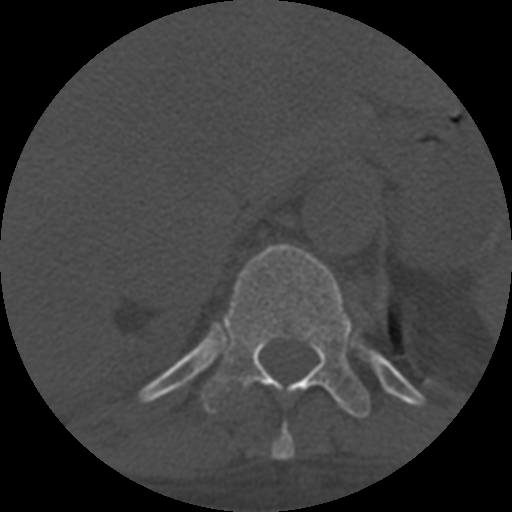
CT including the spine, one axial slice. Position 341 of 708 along the scan axis. Reconstruction kernel STANDARD. One of 3 acquisitions stored at this slice position. Bone window (W 1800 / L 400 HU). 512 × 512 image matrix, field of view 160 × 160 mm. Patient age 55 years. Case-level facts recorded for this patient, not image findings: primary cancer: colon.
Outlined on this slice (semi-automatically segmented with operator editing):
- T10 vertebra: box from (x=271, y=424) to (x=295, y=460) px
- T11 vertebra: (x=202, y=245)–(x=371, y=418)